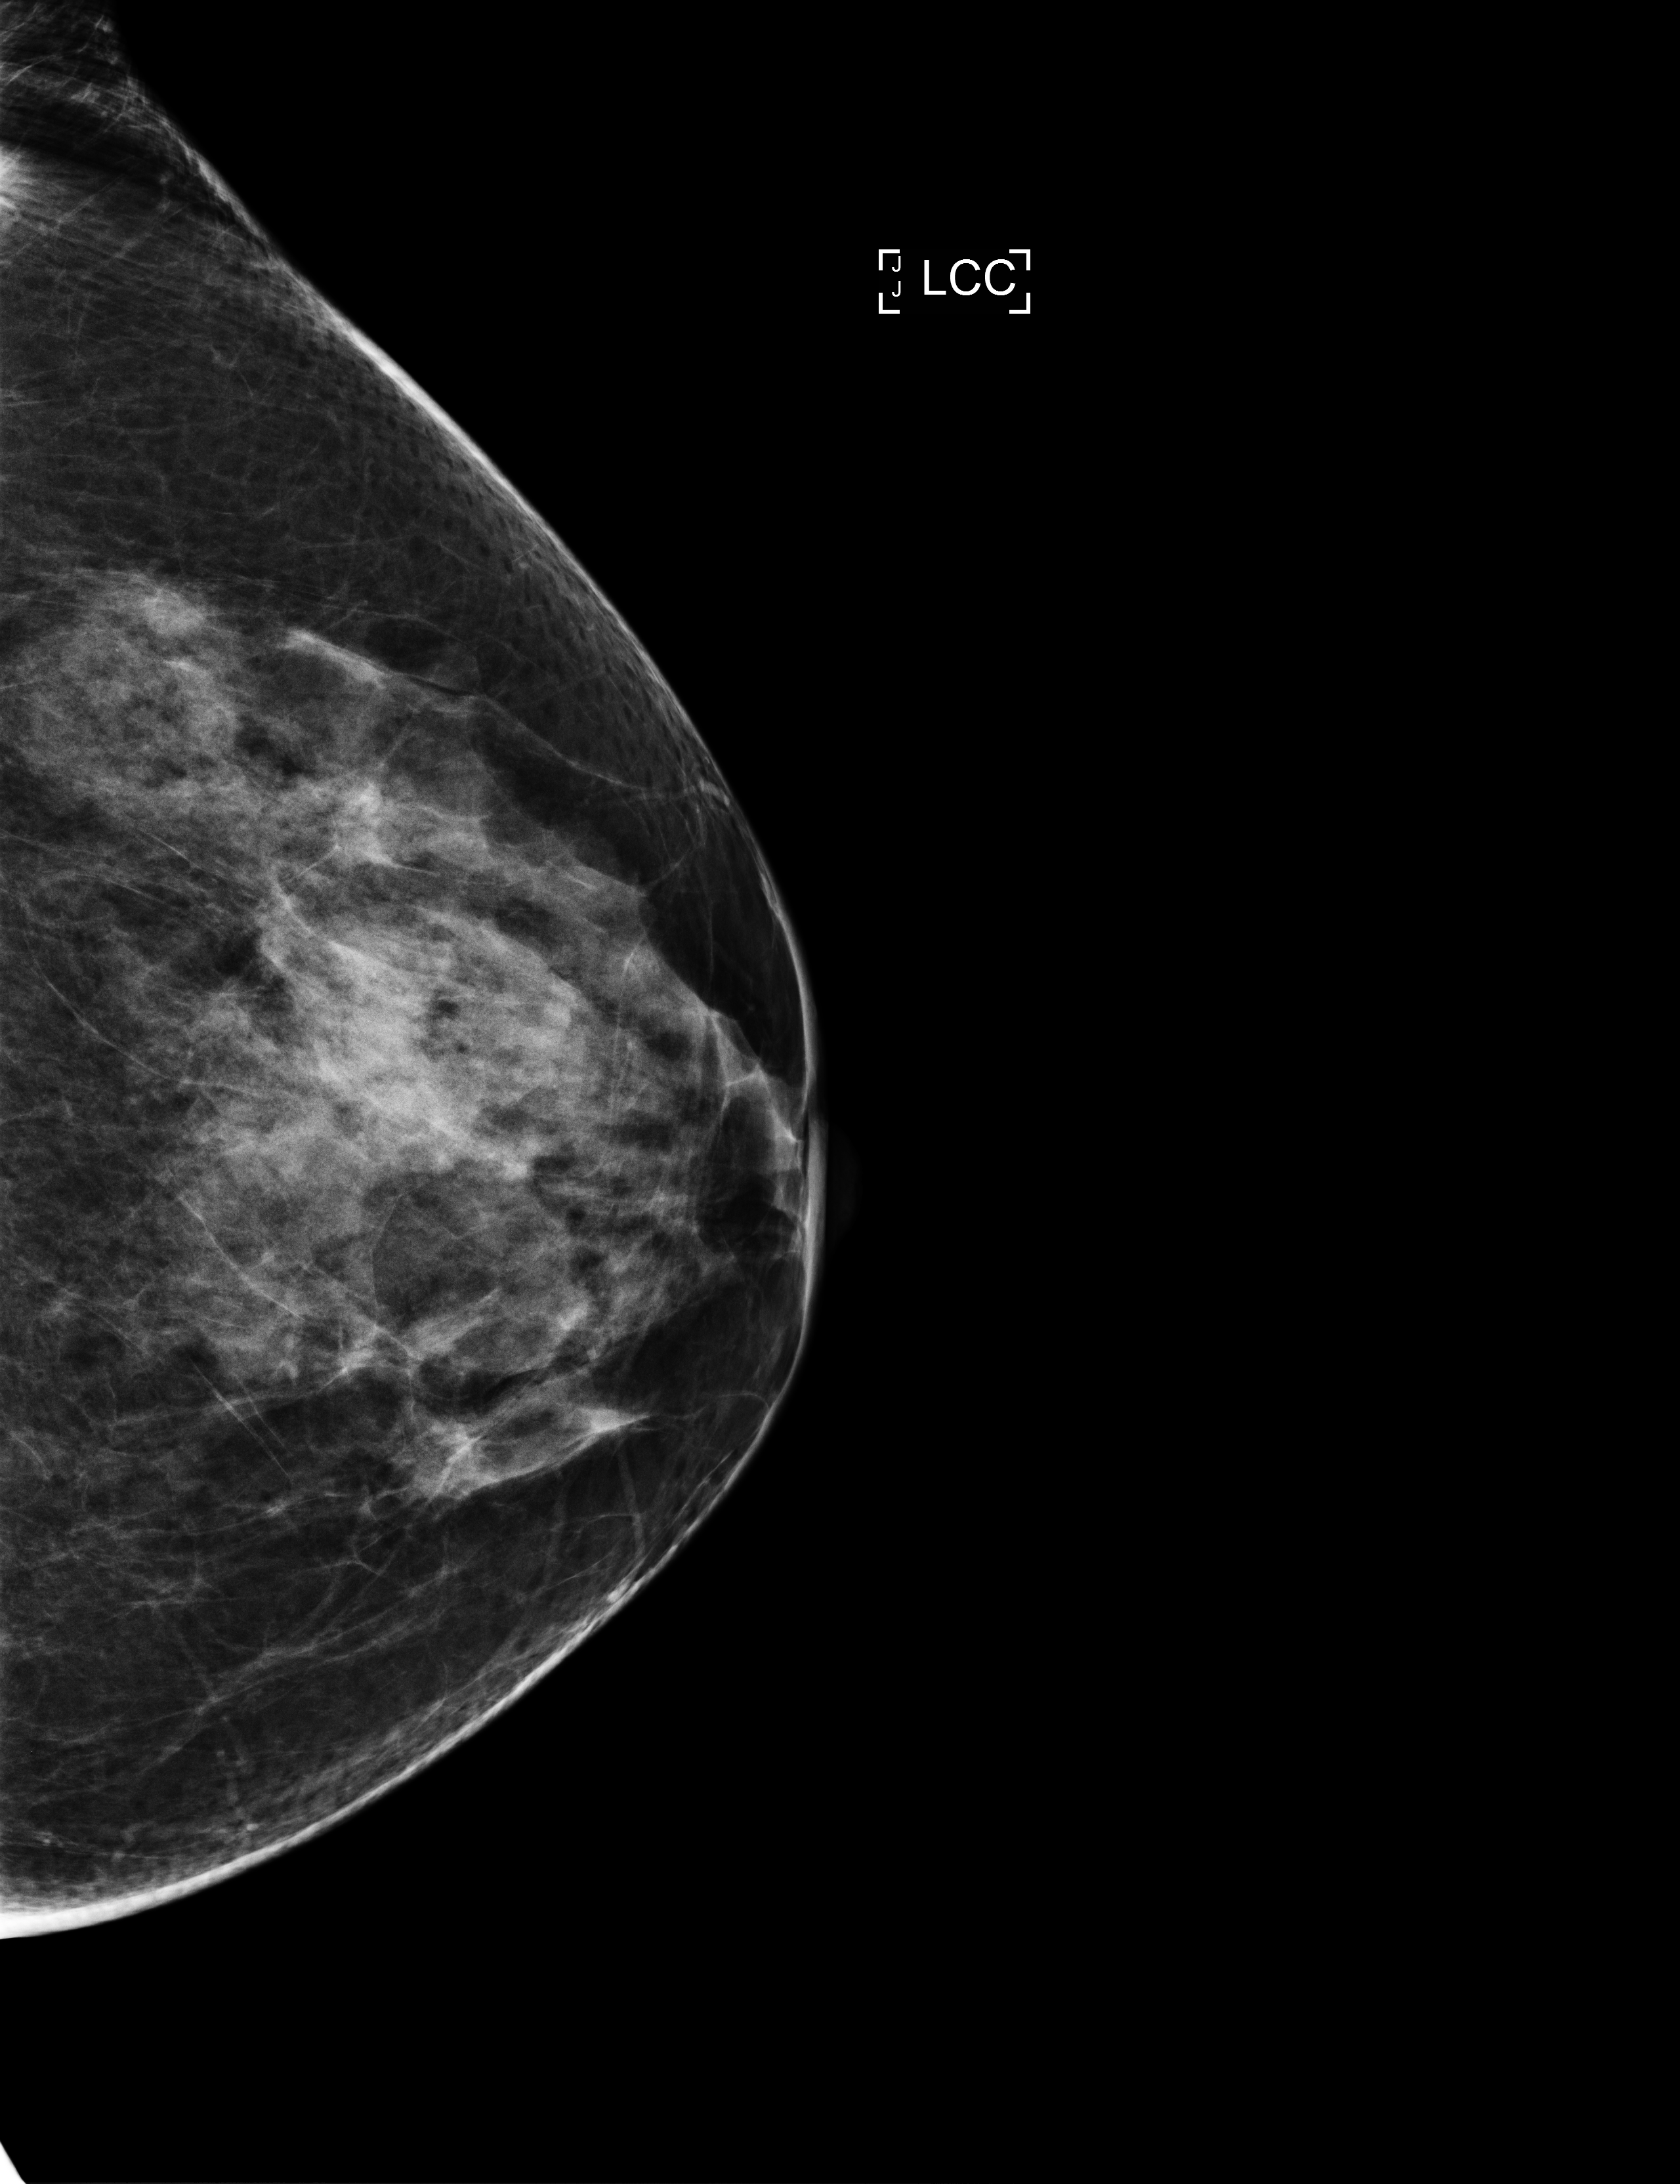
Digital mammogram (FFDM), left breast, cranio-caudal projection, annual screening mammography examination, compressed breast thickness 89 mm, system: Selenia Dimensions. Patient aged 66 years (female).
BI-RADS breast density category at the screening exam (both breasts, scale 1–4): 3. Final BI-RADS assessment for this screening round (tomosynthesis exam, both breasts): category 2. Recall: no recall after this screen.